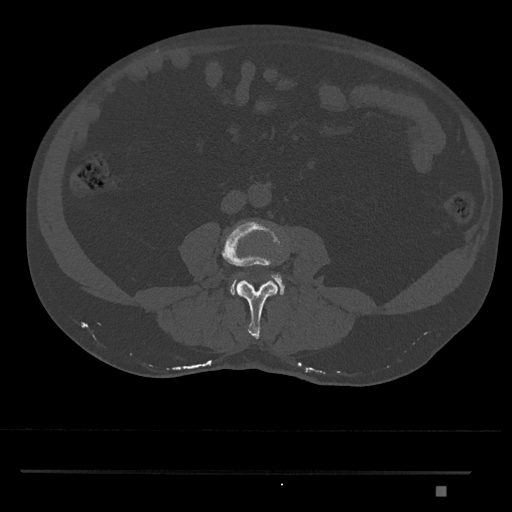
CT including the spine, one axial slice. 120 kVp. Bone window (W 1800 / L 400 HU). 0.5 mm slice thickness. 512 × 512 image matrix. Patient: male, 65 years. From the clinical record (not read from this slice): primary cancer: prostate.
Structures marked on this image (semi-automatically segmented with operator editing):
- L3 vertebra: bounding box (x1, y1, x2, y2) in pixels: (221, 220, 284, 339)
- L4 vertebra: (230, 273, 285, 295)